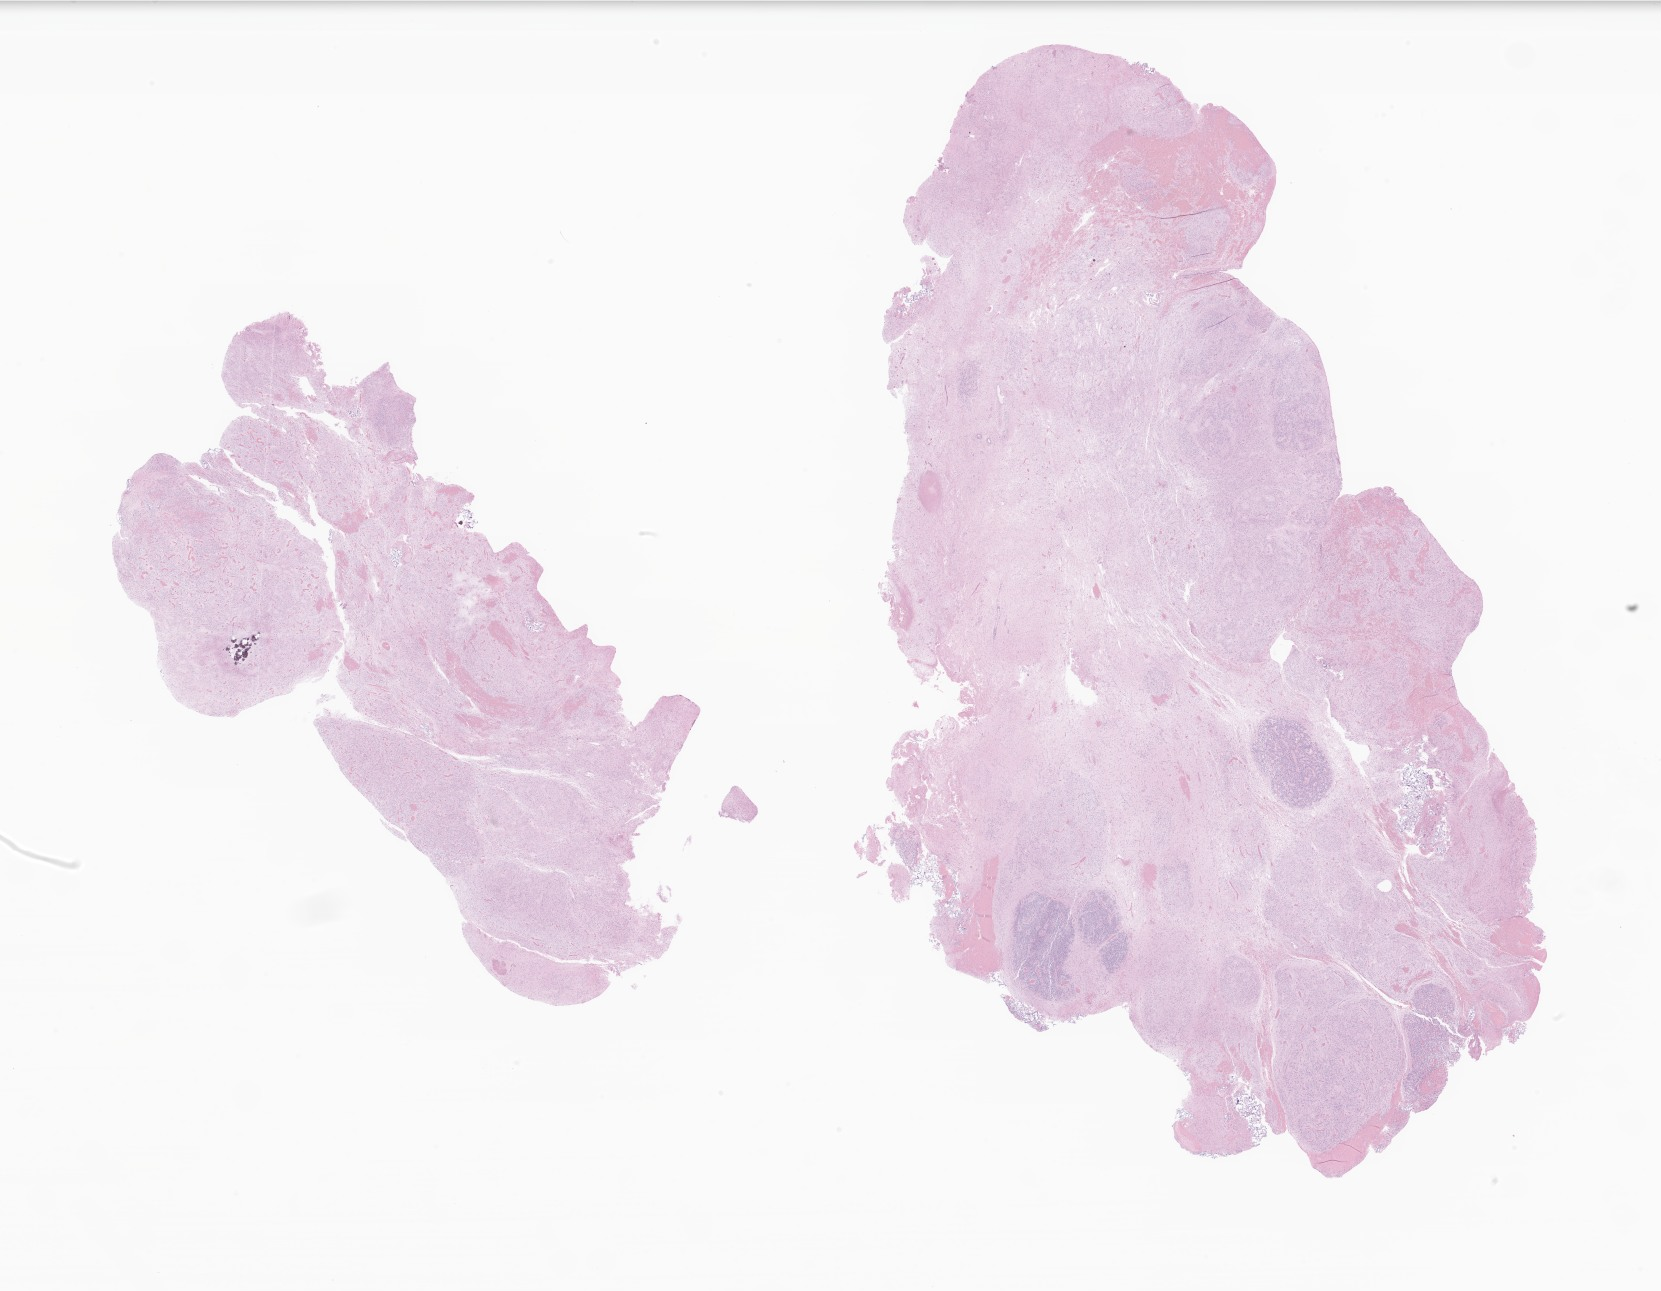
Hematoxylin and eosin (H&E) whole-slide image of tumor tissue from the cerebral ventricle, low-resolution overview of the scanned area, about 27.8 x 21.6 mm; formalin-fixed paraffin-embedded section. Male patient, age 47 months (3 years 11 months).
- diagnosis (ICD-O-3 morphology term): Ependymoma, NOS